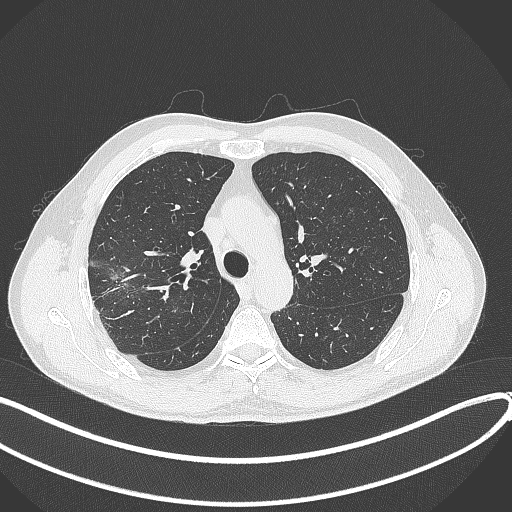
Chest CT, one axial slice; slice 295 of 381 in the series (ordered by position); reconstruction kernel B70f; lung window (W 1500 / L -600 HU); 1 mm slice thickness; 512 × 512 image matrix. Male patient, age 62 years. Case-level facts recorded for this patient, not image findings: clinical TNM (as recorded): T1c N0 M0.
Outlined on this slice (bounding box drawn by a radiologist):
- lung tumour (recorded histology: adenocarcinoma): bounding box <105,268,127,283> (left, top, right, bottom; pixels)